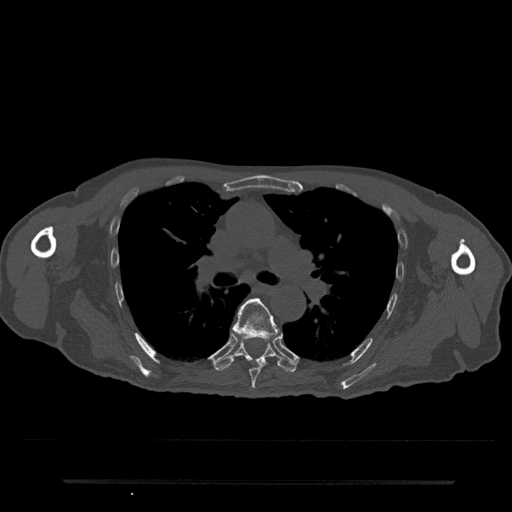
CT including the spine, one axial slice. Slice 507 of 797 in the series (ordered by position). Bone window (W 1800 / L 400 HU). 512 × 512 image matrix. Male patient, age 74 years. From the clinical record (not read from this slice): primary cancer: prostate.
Outlined on this slice (semi-automatic segmentation, software-assisted and operator-edited):
- T6 vertebra: bounding box (x1, y1, x2, y2) in pixels: (231, 298, 279, 389)
- T7 vertebra: (215, 340, 297, 372)